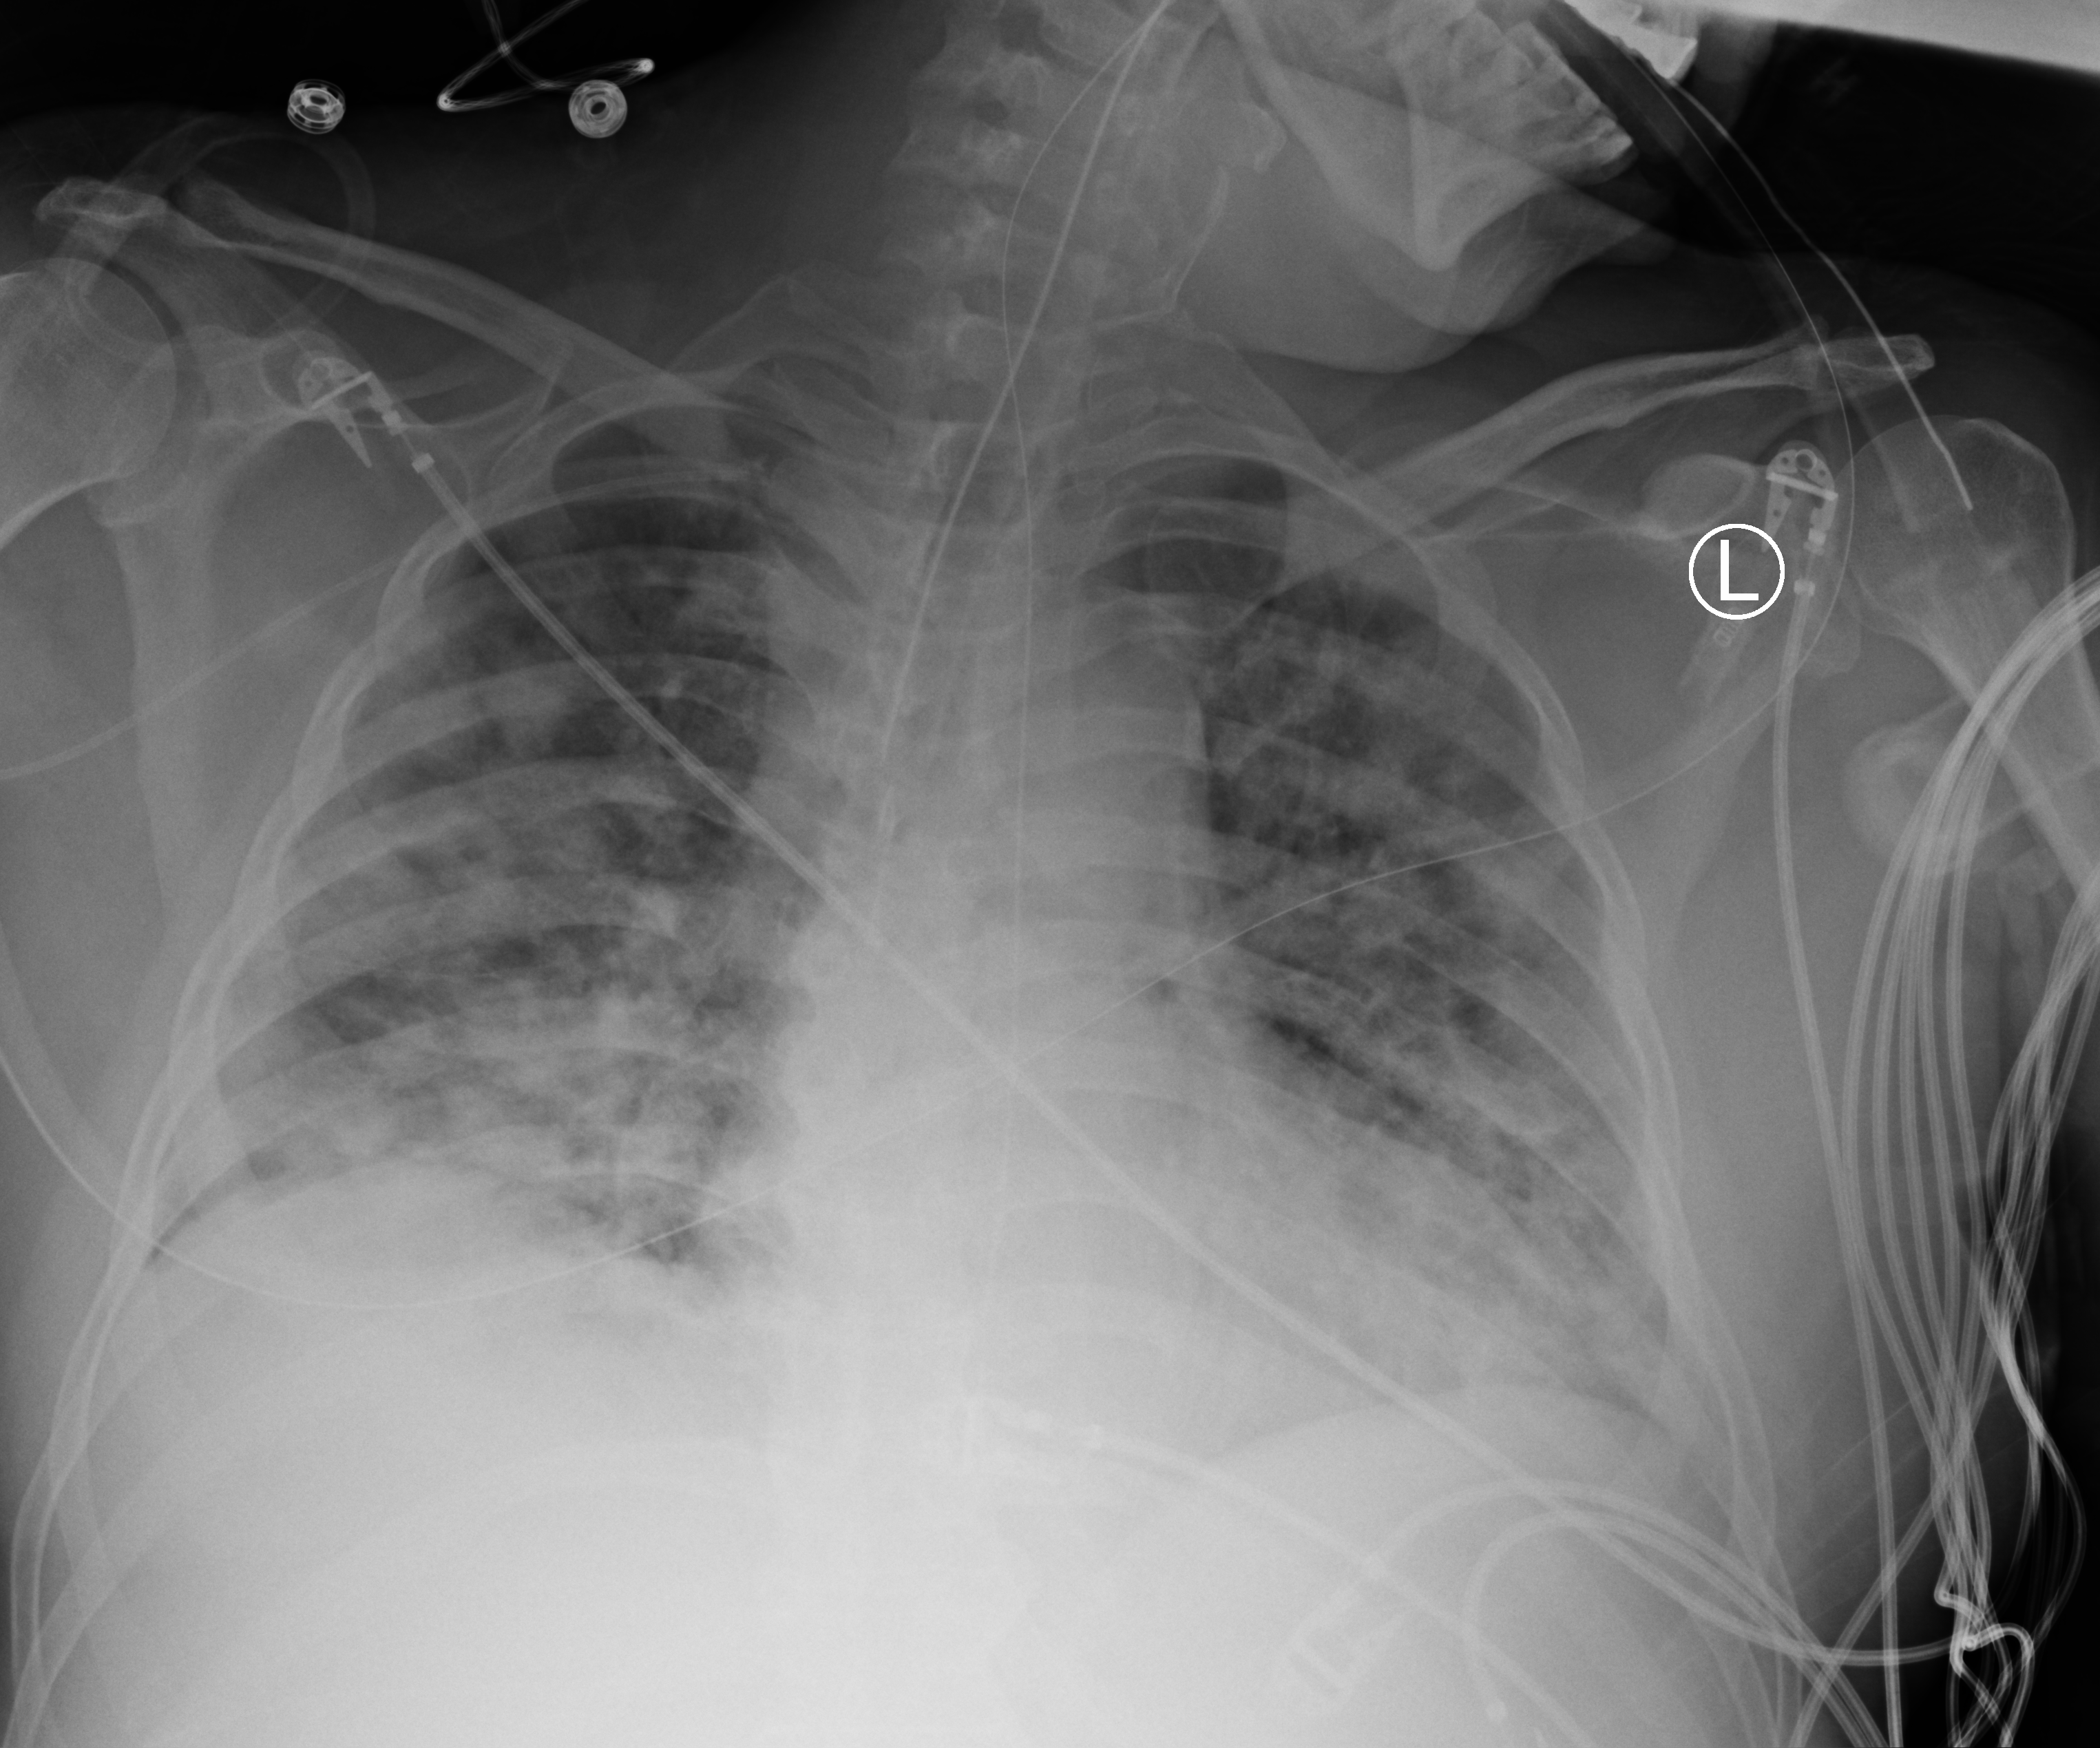
Chest X-ray (portable); anteroposterior (AP) projection. Patient hospitalised with COVID-19; male, aged 18–59 years.
Admission-level facts for this patient (not findings on this image; timing relative to this image not recorded):
- other chronic lung disease (admission record): no
- mechanically ventilated during this hospital stay: yes
- admitted to intensive care during this hospital stay: yes